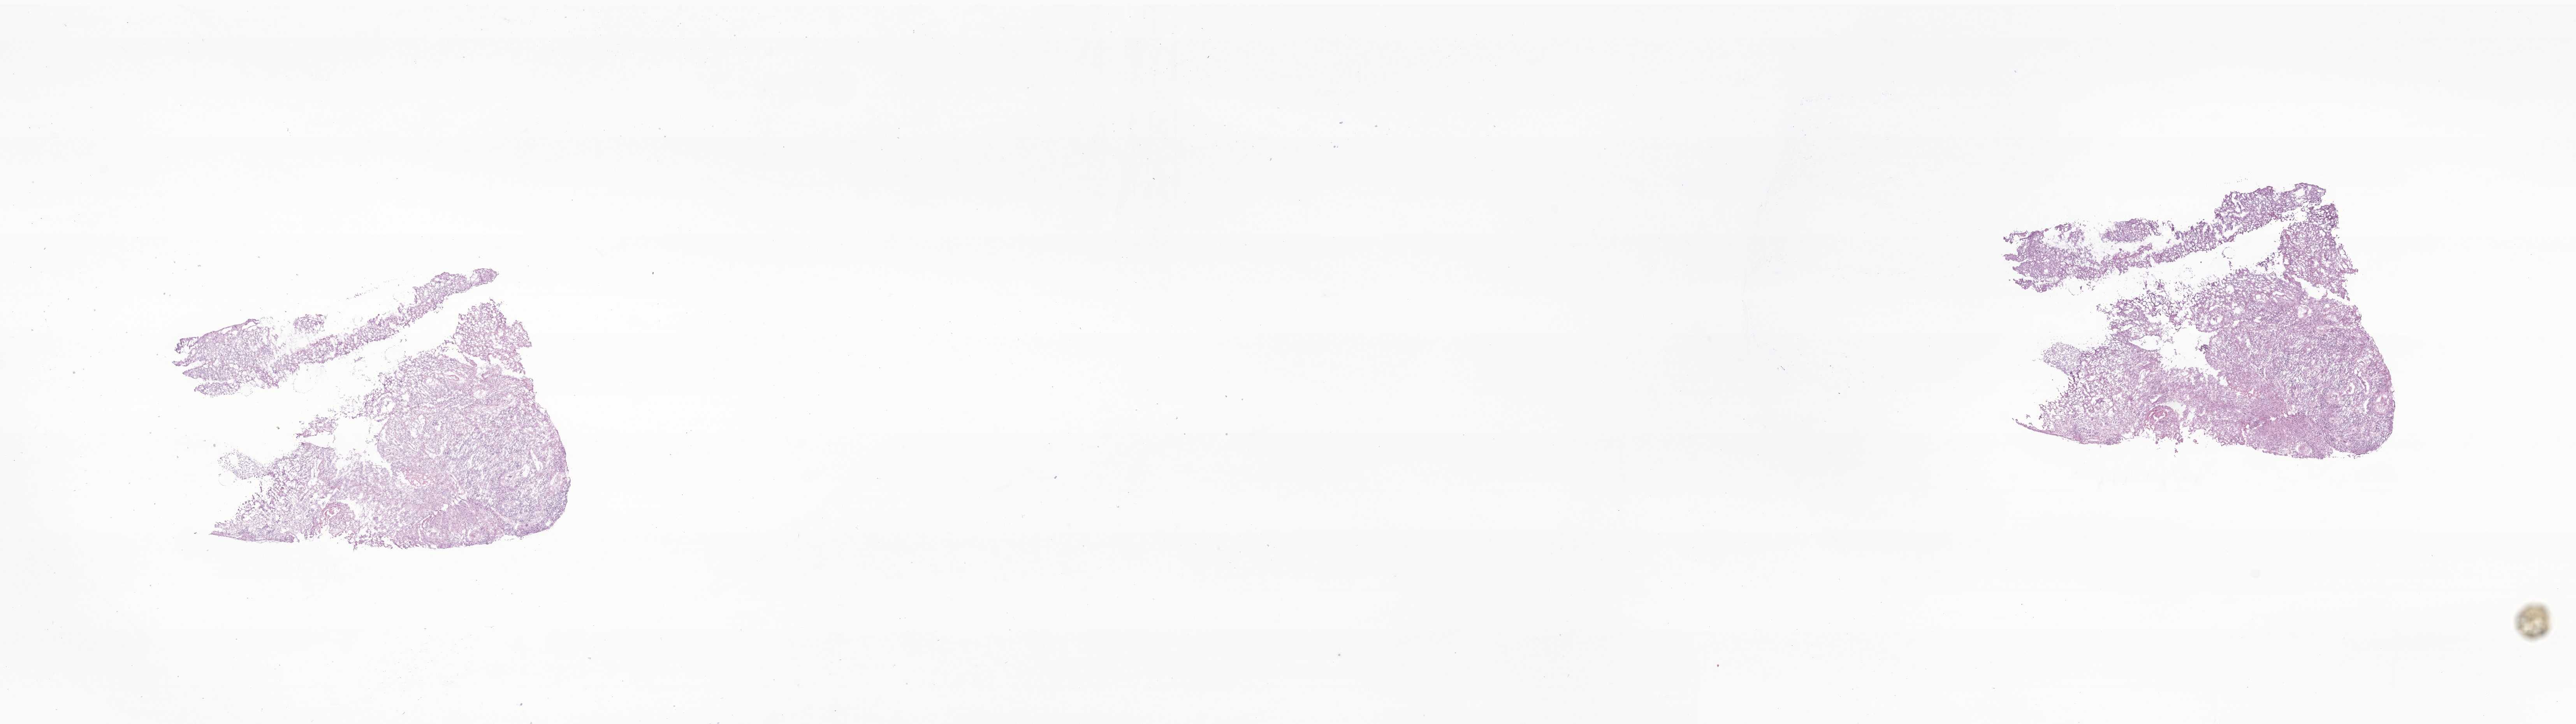
H&E whole-slide image of tumor tissue from the brain — a low-resolution overview of the entire scanned area, about 27.9 x 7.8 mm; frozen section. Patient: female, age 114 months.
Diagnosis (ICD-O-3 morphology term): Neoplasm, uncertain whether benign or malignant.